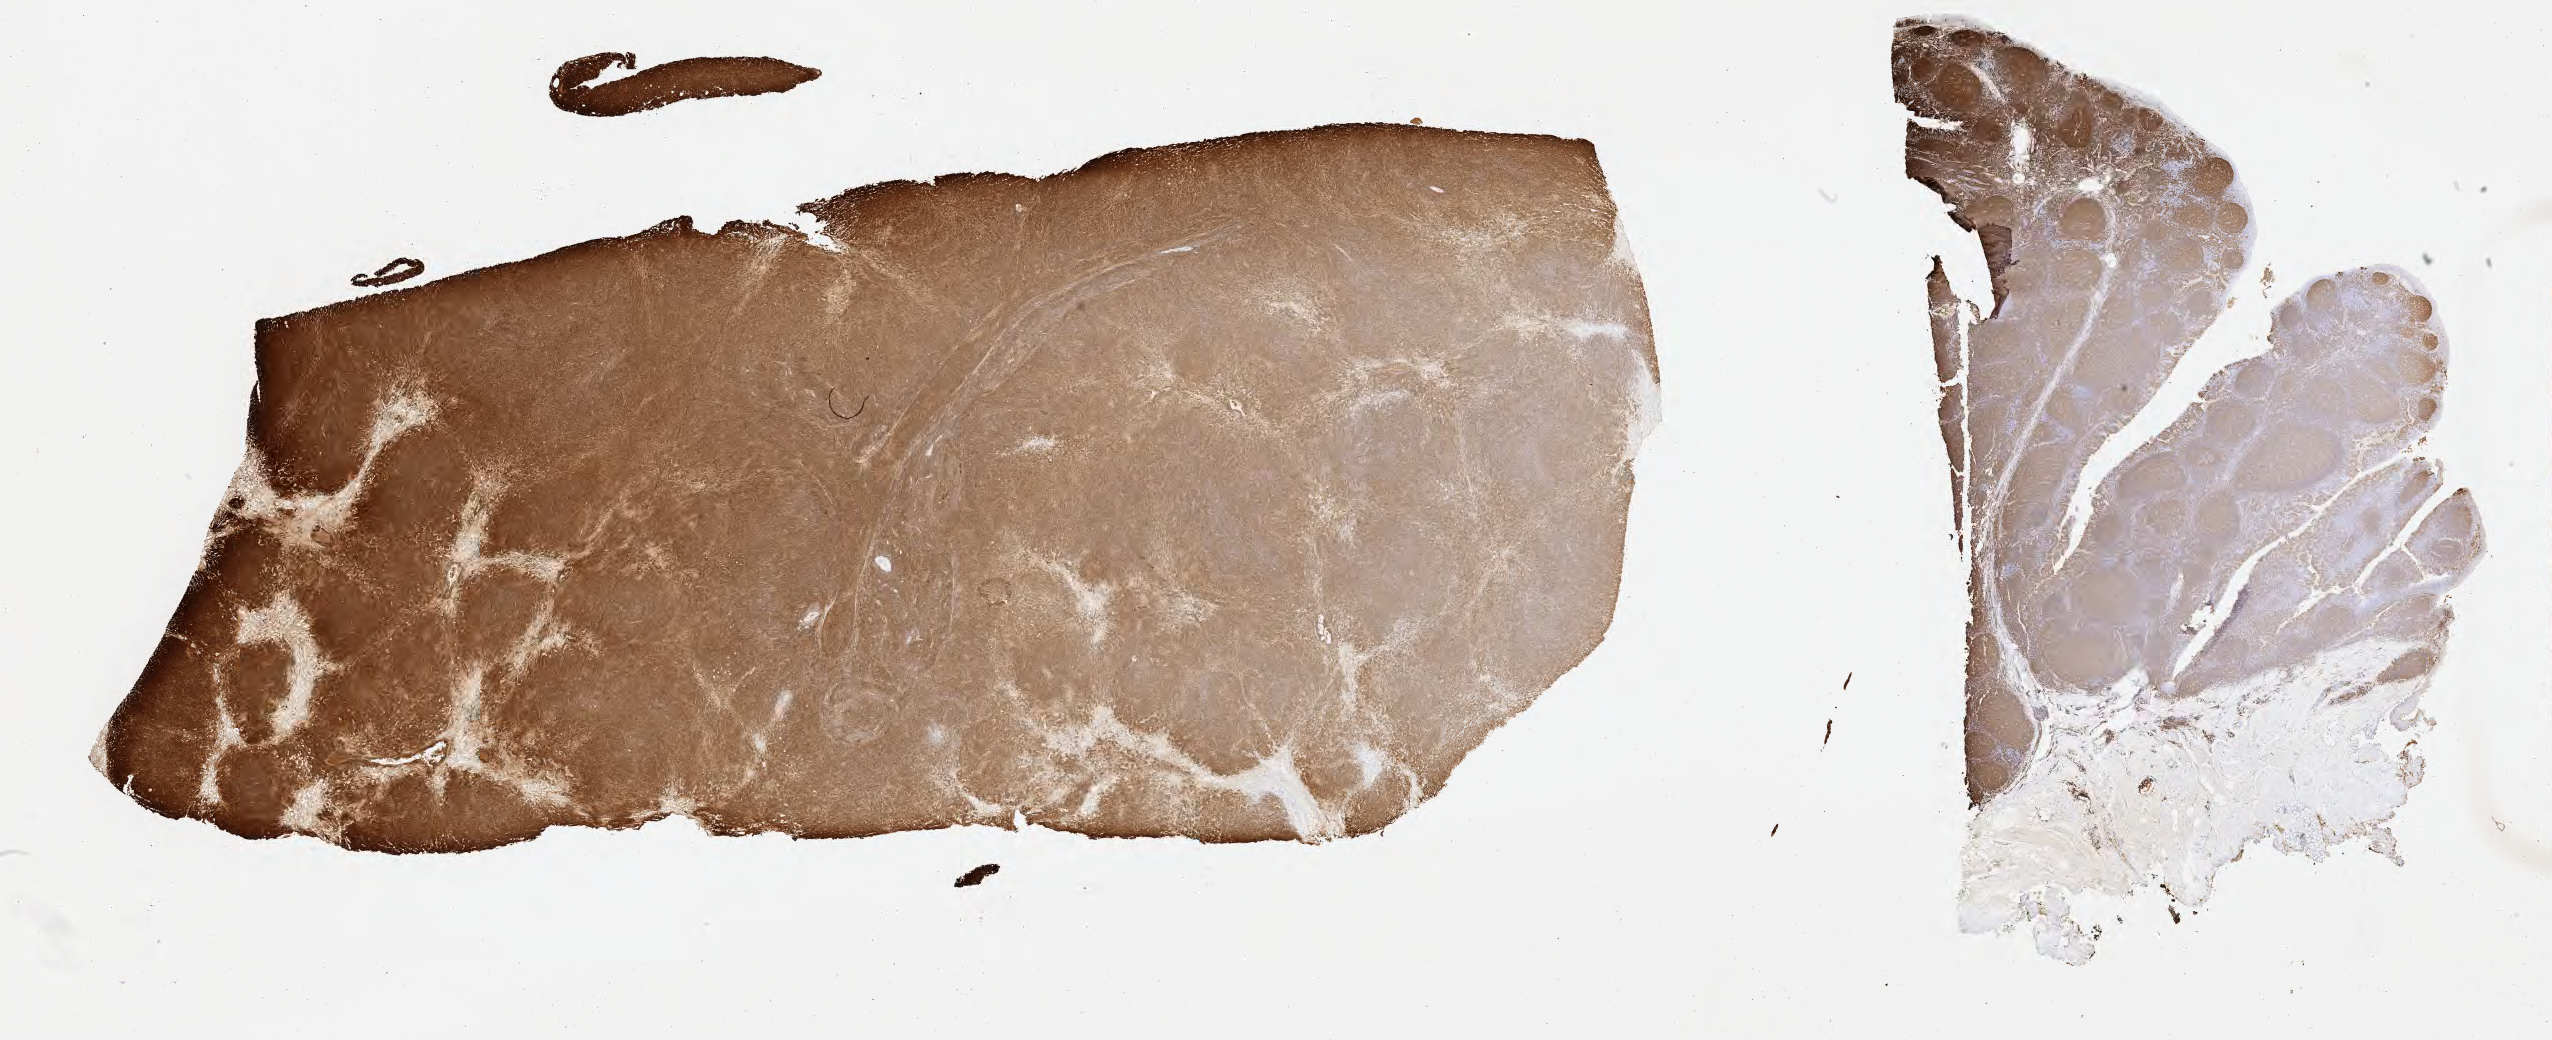
IHC for CD20, whole-slide image — shown as a low-resolution overview of the whole scanned area (about 41.3 x 16.8 mm); tumor tissue. Male patient, age 39 years.
• histologic diagnosis: Diffuse large B-cell lymphoma, NOS